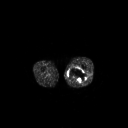
FDG PET of an extremity soft-tissue mass (from a PET/CT study), one axial slice; slice 221 of 267 in the series (ordered by position); 3.27 mm slice thickness; 128 × 128 image matrix. Male patient, age 44 years. Case-level facts recorded for this patient, not image findings: histological type: undifferentiated pleomorphic liposarcoma; grade: high; site of the primary tumour: left thigh.
Structures marked on this image (expert contour drawn on MRI and transferred to this co-registered scan by the dataset authors):
- gross tumour volume including surrounding oedema: box from (x=68, y=67) to (x=87, y=83) px
- gross tumour volume (mass): (x=68, y=67)–(x=87, y=83)